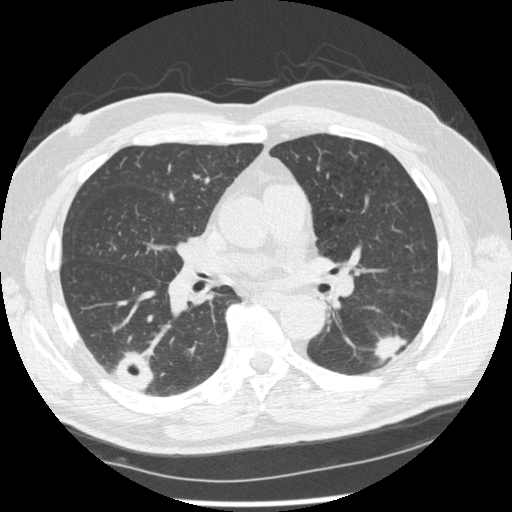
Axial slice from a low-dose chest CT screening exam; second screening round (one year after baseline); lung window (W 1500 / L -600 HU); 1.25 mm slice thickness; 512 × 512 image matrix, field of view 360 × 360 mm. Male, age 74 years at enrolment.
Lesion marked by an expert reader, bounding box (x1, y1, x2, y2) in pixels: (369, 315, 422, 369). The screening reader recorded 7 non-calcified nodules or masses ≥4 mm on this exam (right upper lobe, right lower lobe, right upper lobe, right lower lobe, left lower lobe, left upper lobe, left upper lobe); which of them this box marks is not recorded. Participant outcome: lung cancer diagnosed 43 days after this screen — squamous cell carcinoma, NOS, left lower lobe, well differentiated (G1), stage IA (AJCC 6th edition), 28 mm at pathology.